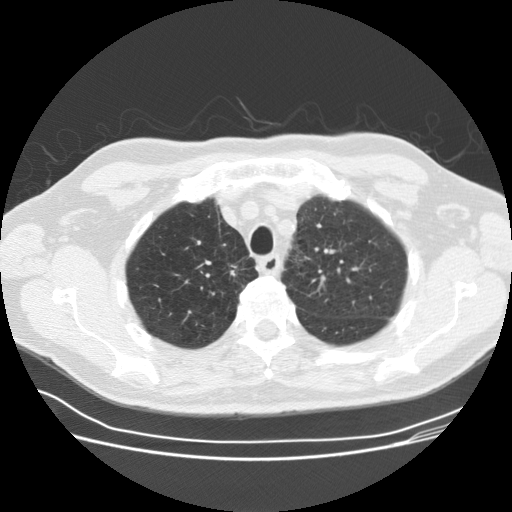
Low-dose screening chest CT, one axial slice. Position 128 of 164 along the scan axis. 120 kVp. Lung window (W 1500 / L -600 HU). 2.5 mm slice thickness. 512 × 512 image matrix, field of view 360 × 360 mm.
Annotated regions visible in this slice (expert manual segmentation):
- lesion 1 (tumor, upper lobe of right lung): bounding box <228,263,239,276> (left, top, right, bottom; pixels)